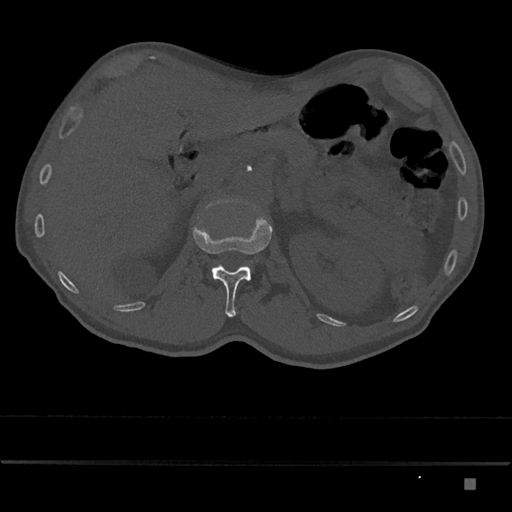
CT including the spine, one axial slice. Position 532 of 797 along the scan axis. Reconstruction kernel Br40s/3. 120 kVp. Bone window (W 1800 / L 400 HU). 512 × 512 image matrix, field of view 390 × 390 mm. Male patient, age 72 years. From the clinical record (not read from this slice): primary cancer: prostate.
Outlined on this slice (semi-automatic segmentation, software-assisted and operator-edited):
- L1 vertebra: box from (x=192, y=217) to (x=272, y=317) px